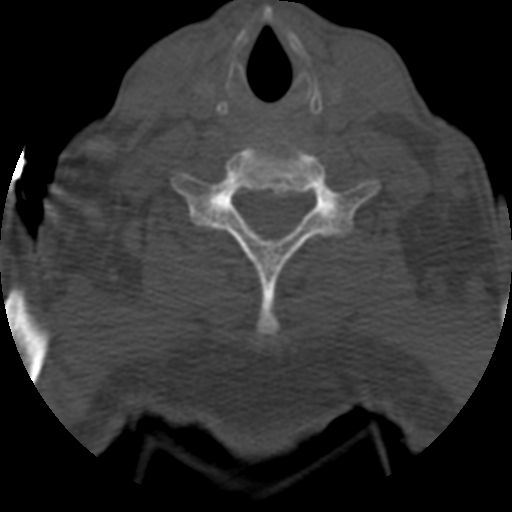
CT including the spine, one axial slice; position 532 of 708 along the scan axis; 120 kVp; one of 3 acquisitions stored at this slice position; bone window (W 1800 / L 400 HU); 512 × 512 image matrix, field of view 160 × 160 mm. Patient age 55 years. From the clinical record (not read from this slice): primary cancer: colon.
Outlined on this slice (semi-automatically segmented with operator editing):
- T1 vertebra: box from (x=222, y=199) to (x=241, y=221) px